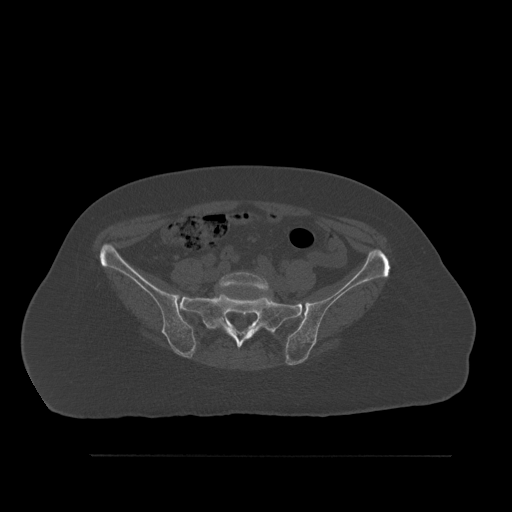
CT including the spine, one axial slice; slice 176 of 527 in the series (ordered by position); bone window (W 1800 / L 400 HU); 512 × 512 image matrix, field of view 470 × 470 mm. Patient: female, 73 years. From the clinical record (not read from this slice): primary cancer: breast.
Annotated regions visible in this slice (semi-automatic segmentation, software-assisted and operator-edited):
- L5 vertebra: box from (x=216, y=272) to (x=272, y=329) px